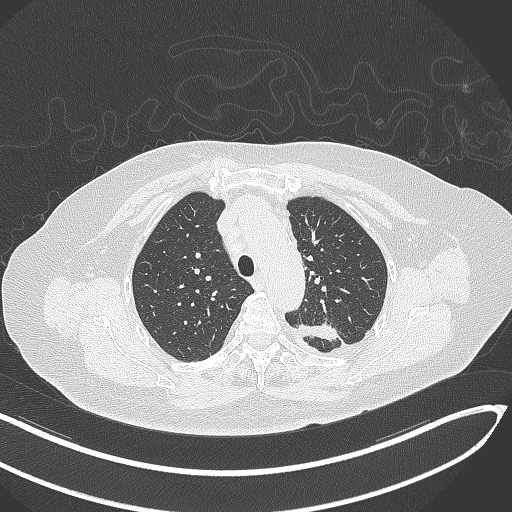
Chest CT, one axial slice. Slice 240 of 270 in the series (ordered by position). 120 kVp. Lung window (W 1500 / L -600 HU). 1 mm slice thickness. 512 × 512 image matrix, field of view 400 × 400 mm. Patient: female, 76 years. Case-level facts recorded for this patient, not image findings: clinical TNM (as recorded): T1c N0 M0.
Outlined on this slice (bounding box drawn by a radiologist):
- lung tumour (recorded histology: adenocarcinoma): bounding box <299,320,339,344> (left, top, right, bottom; pixels)